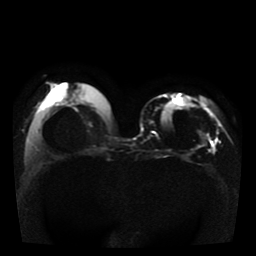
Breast MRI, one axial slice. Position 15 of 41 along the scan axis. Diffusion-weighted series; image 2 of 4 stored at this slice position (different b-values; order by instance number). 1.5 T. 256 × 256 image matrix. Female patient.
Structures marked on this image (expert manual segmentation):
- tumour on diffusion-weighted imaging: box from (x=201, y=134) to (x=209, y=146) px